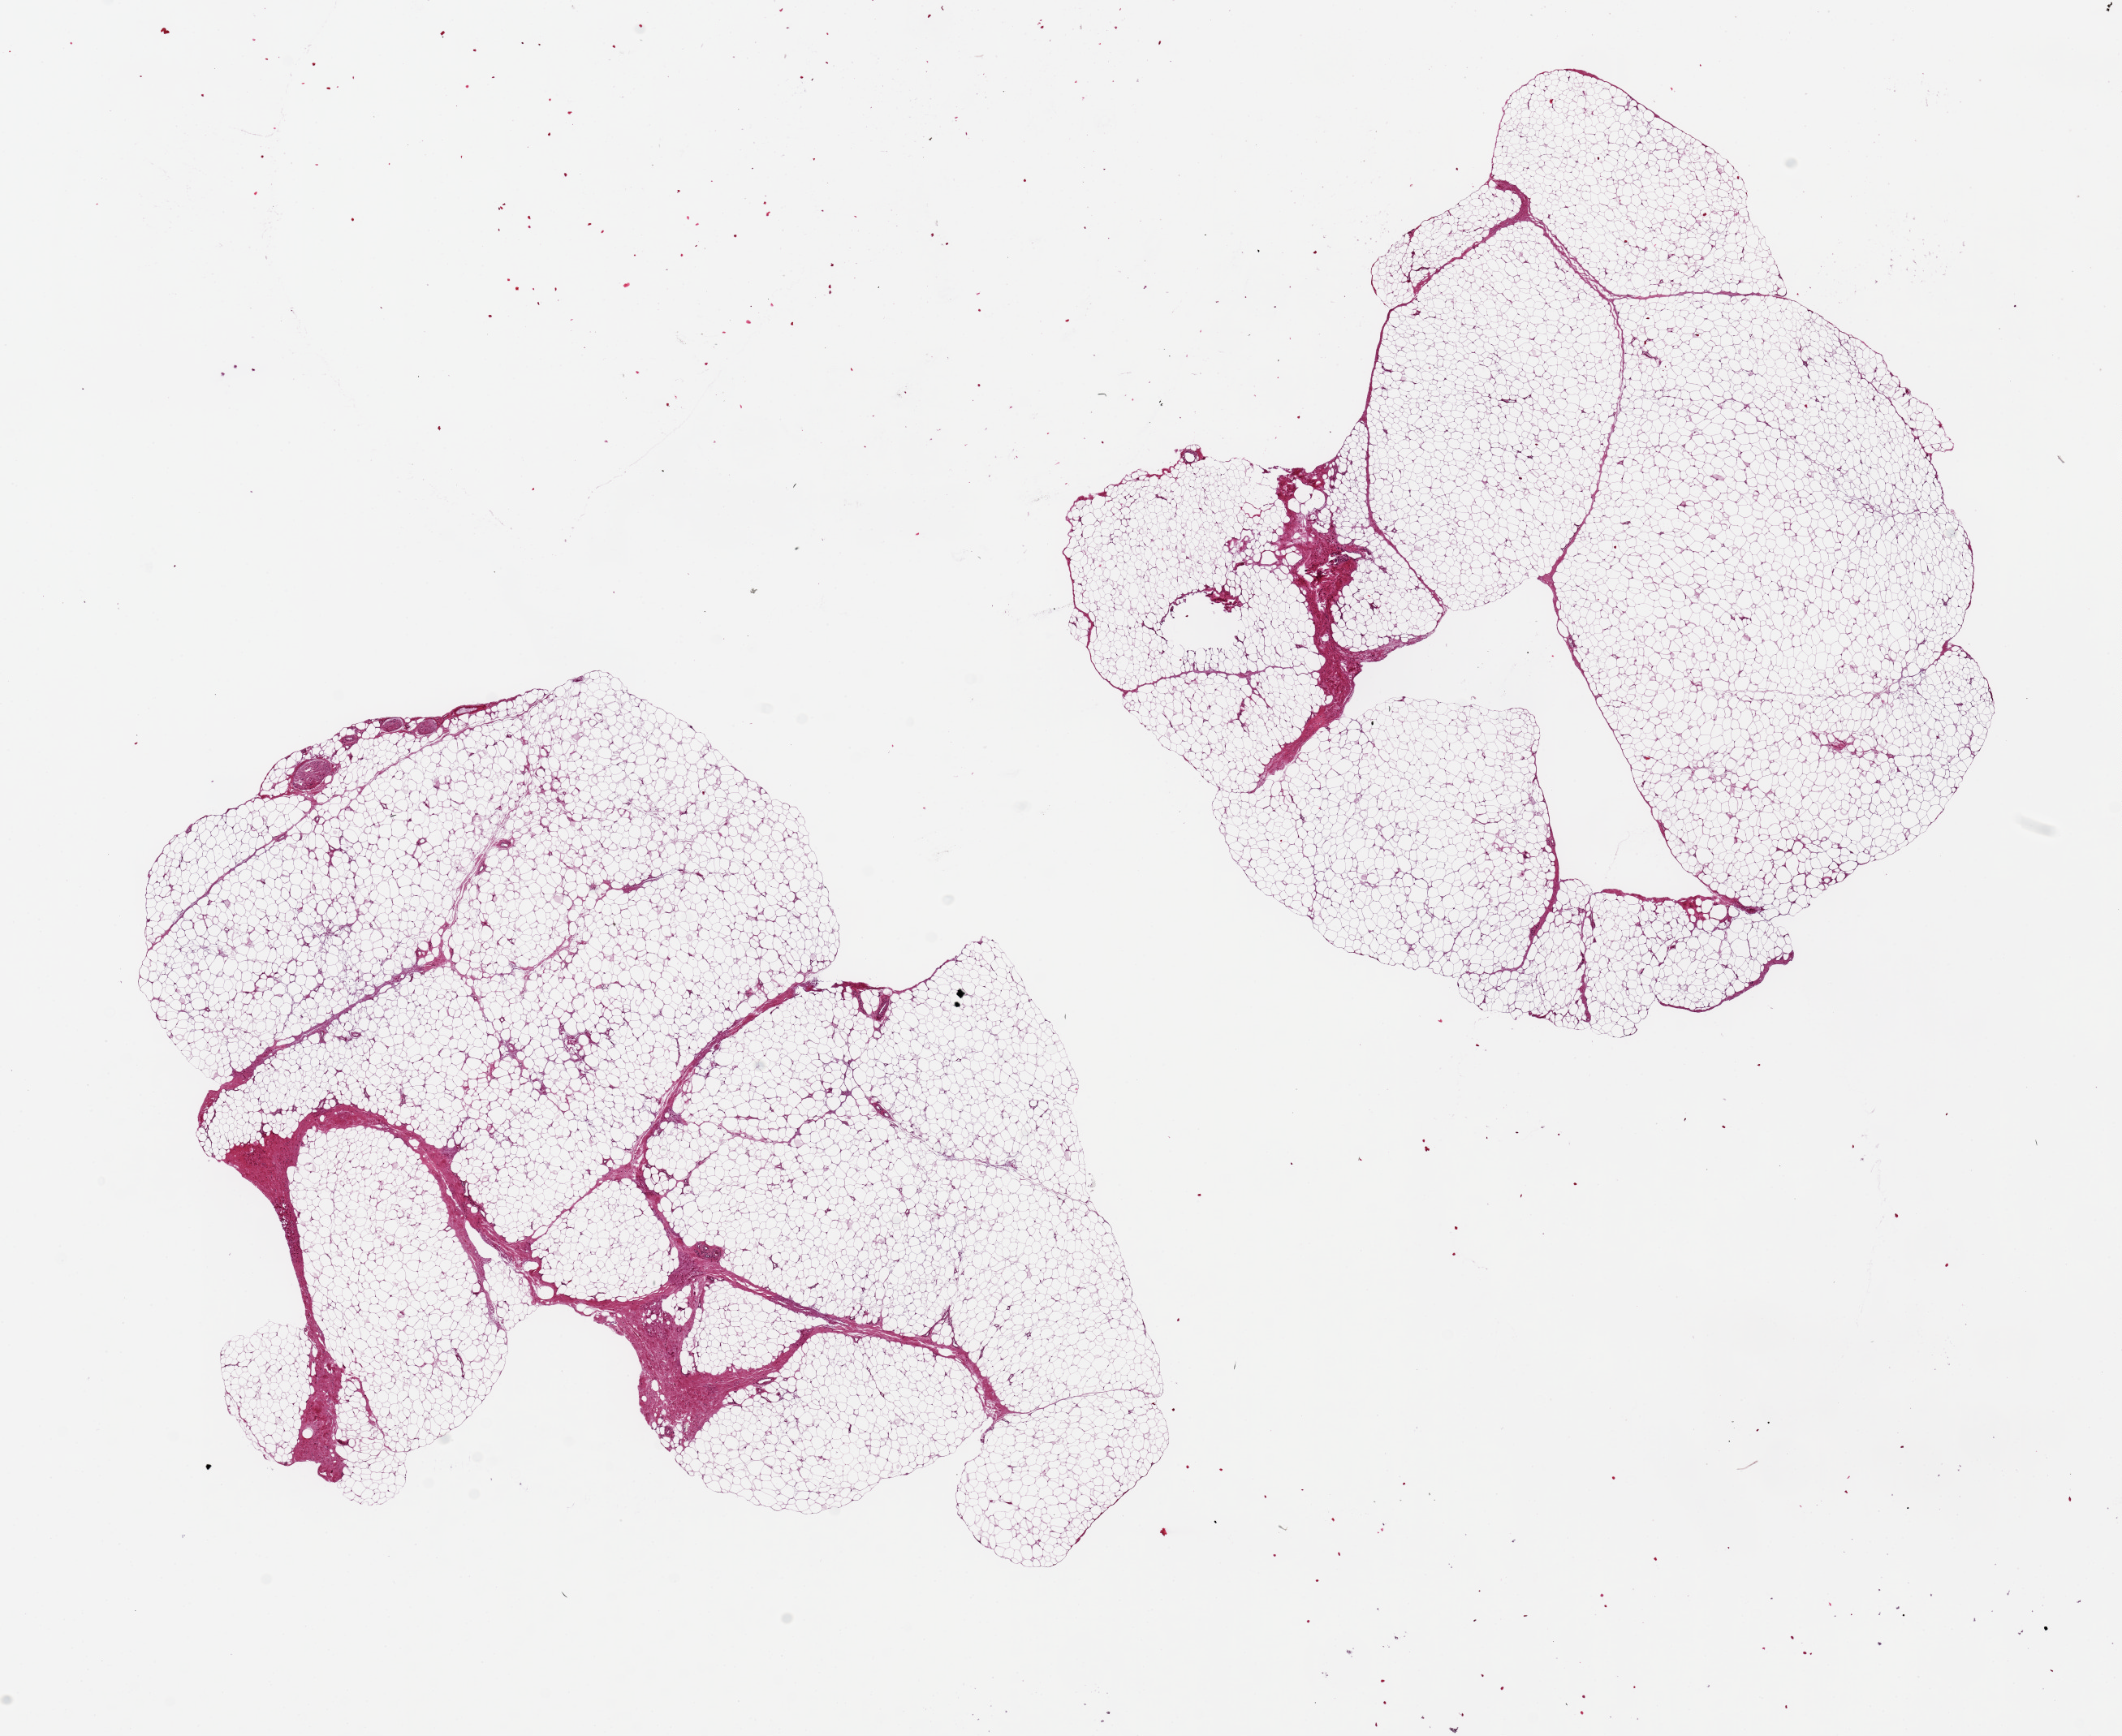
Haematoxylin and eosin whole-slide image, brightfield, a low-resolution overview of the entire scanned area, about 20.7 x 16.9 mm, PAXgene-fixed paraffin-embedded (PFPE) section, section of adipose tissue (target tissue), tissue donor sample. Donor sex: female.
Pathologist's review note for this sample: 2 pieces. 11x8 & 9x8mm; well preserved.